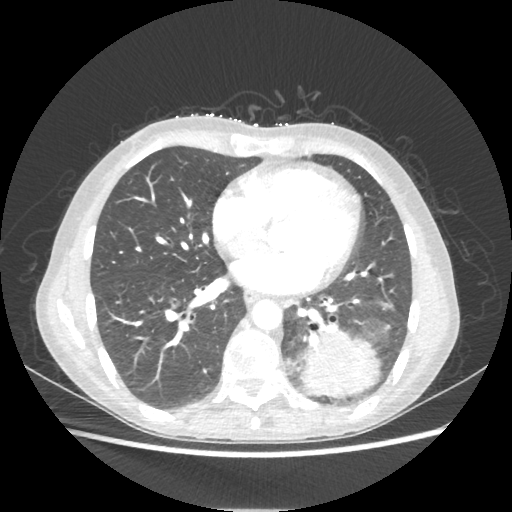
Chest CT, one axial slice. Slice 90 of 221 in the series (ordered by position). Reconstruction kernel STANDARD. Lung window (W 1500 / L -600 HU). 1.25 mm slice thickness. 512 × 512 image matrix, field of view 360 × 360 mm. Female patient, age 53 years. From the clinical record (not read from this slice): clinical TNM (as recorded): T3 N0 M0.
Outlined on this slice (bounding box drawn by a radiologist):
- lung tumour (recorded histology: adenocarcinoma): bounding box <298,327,378,396> (left, top, right, bottom; pixels)